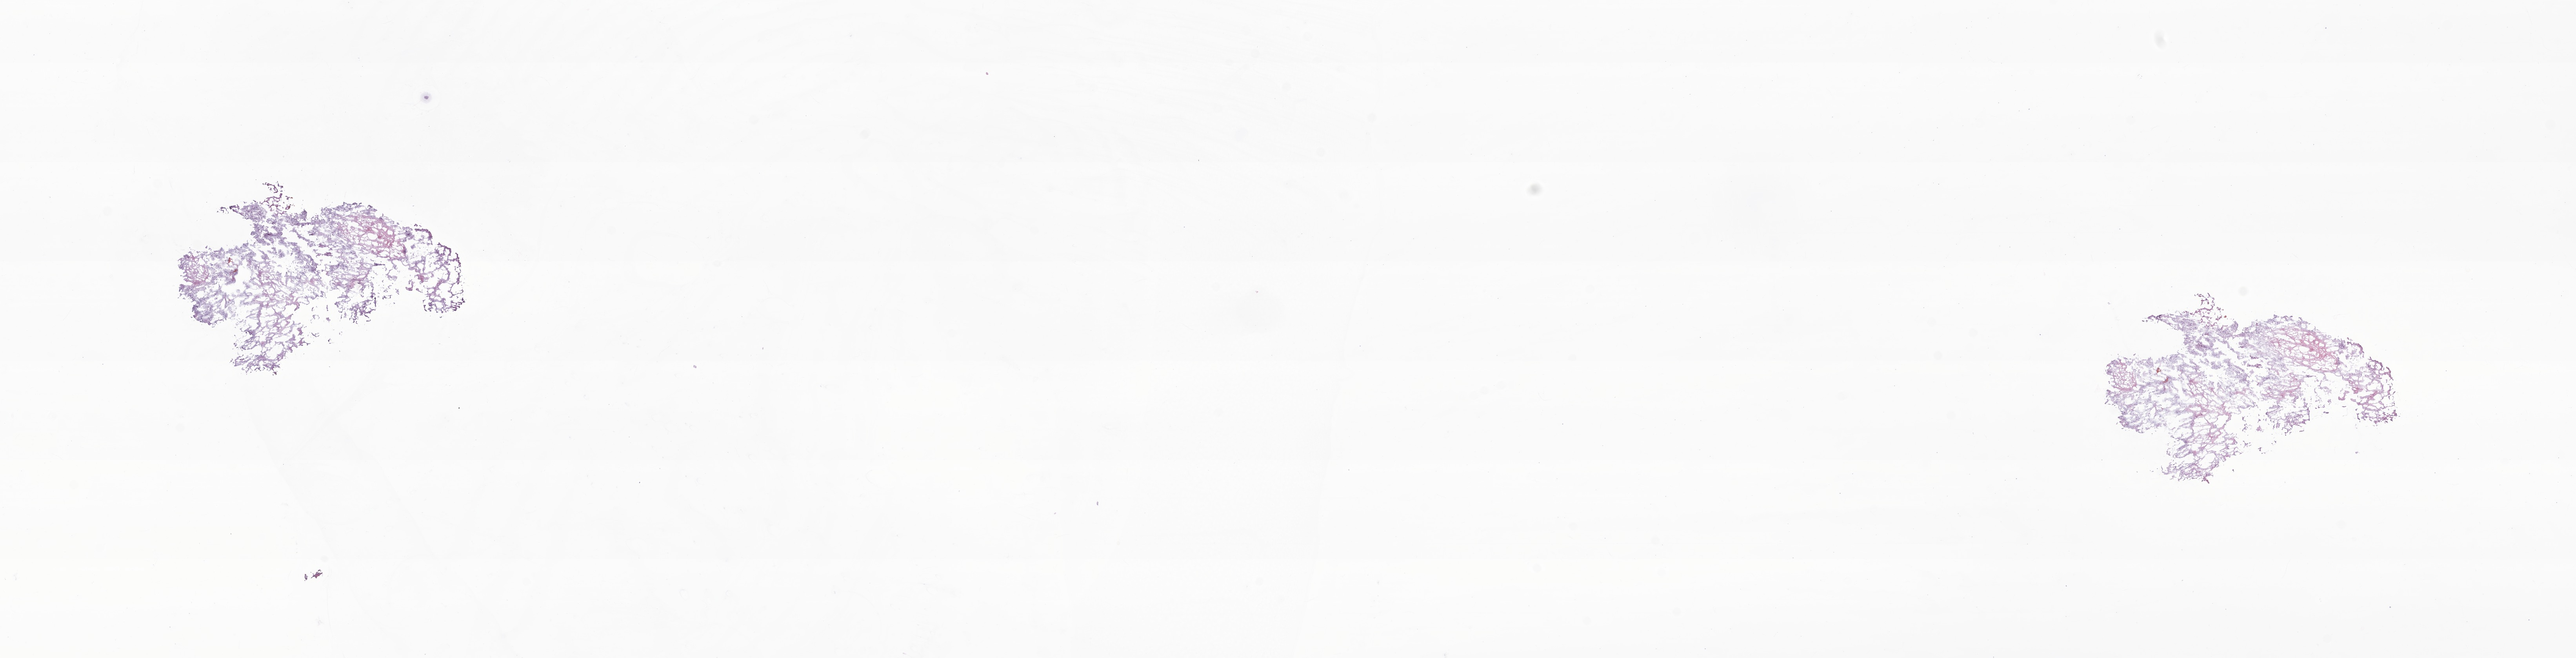
Haematoxylin and eosin whole-slide image of tumor tissue from the brain — a low-resolution overview of the entire scanned area, about 27.6 x 7.1 mm, frozen section (OCT-embedded). Patient female; age 203 months.
• diagnosis: Neoplasm, uncertain whether benign or malignant